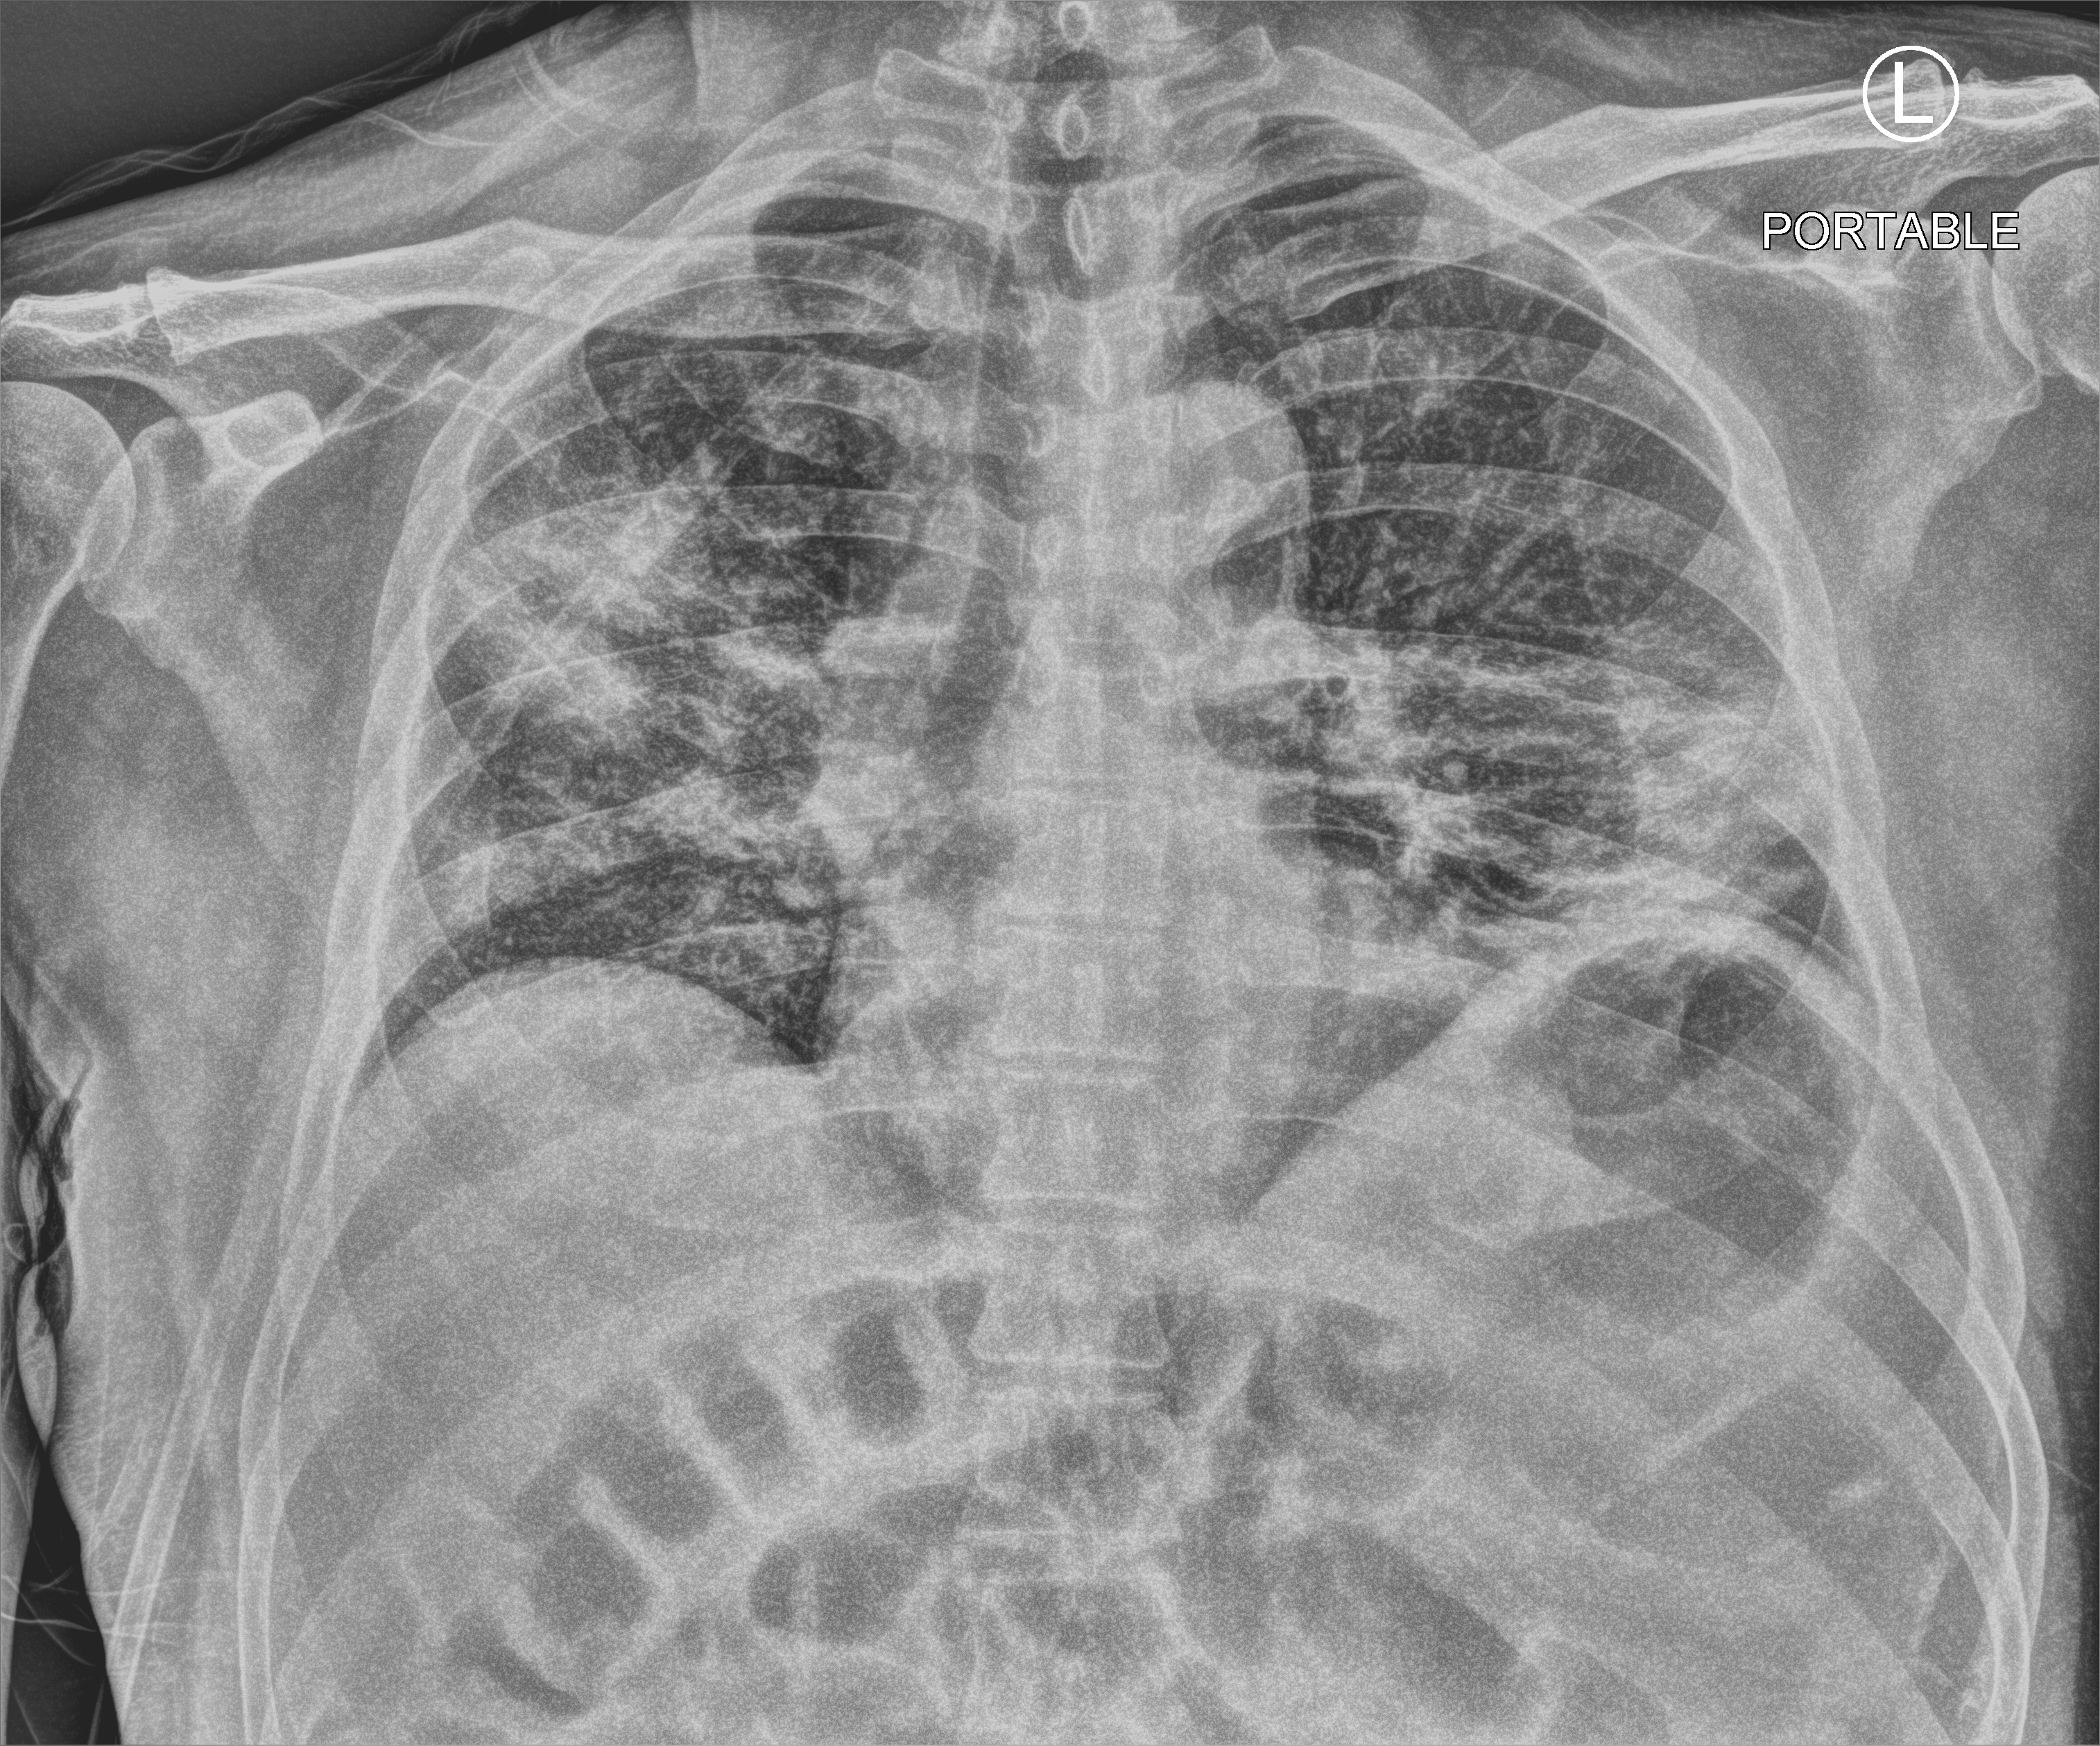
Bedside chest radiograph (computed radiography), anteroposterior (AP) projection. Patient hospitalised with COVID-19; male, aged 60–74 years.
Admission-level facts for this patient (not findings on this image; timing relative to this image not recorded):
- mechanically ventilated during this hospital stay: no
- chronic kidney disease (admission record): no